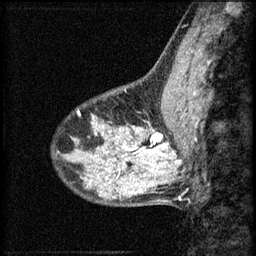
Breast MRI (dynamic contrast-enhanced), one sagittal slice. Slice 18 of 60 in the series (ordered by position). 3 images stored at this slice position (order not interpretable as contrast timing). 1.5 T. TE 4.2 ms, TR 8.2 ms. 256 × 256 image matrix, field of view 180 × 180 mm. Female patient, age 40 years.
Structures marked on this image (semi-automatically segmented with operator editing):
- analysis volume of interest (the breast-tissue region the enhancement analysis was run in; not a lesion): bounding box [x1, y1, x2, y2] px = [108, 108, 167, 159]
- tumour enhancement mask (voxels above the 70 % enhancement threshold inside the analysis volume of interest): [122, 134, 165, 157]